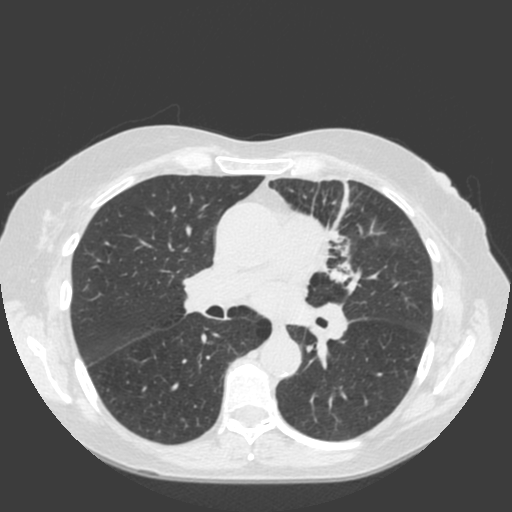
Low-dose screening chest CT, one axial slice; 120 kVp; lung window (W 1500 / L -600 HU); 2 mm slice thickness; 512 × 512 image matrix, field of view 350 × 350 mm.
Outlined on this slice (manually delineated by an expert):
- lesion 1 (tumor, hilum of left lung): bounding box [x1, y1, x2, y2] px = [325, 229, 356, 288]